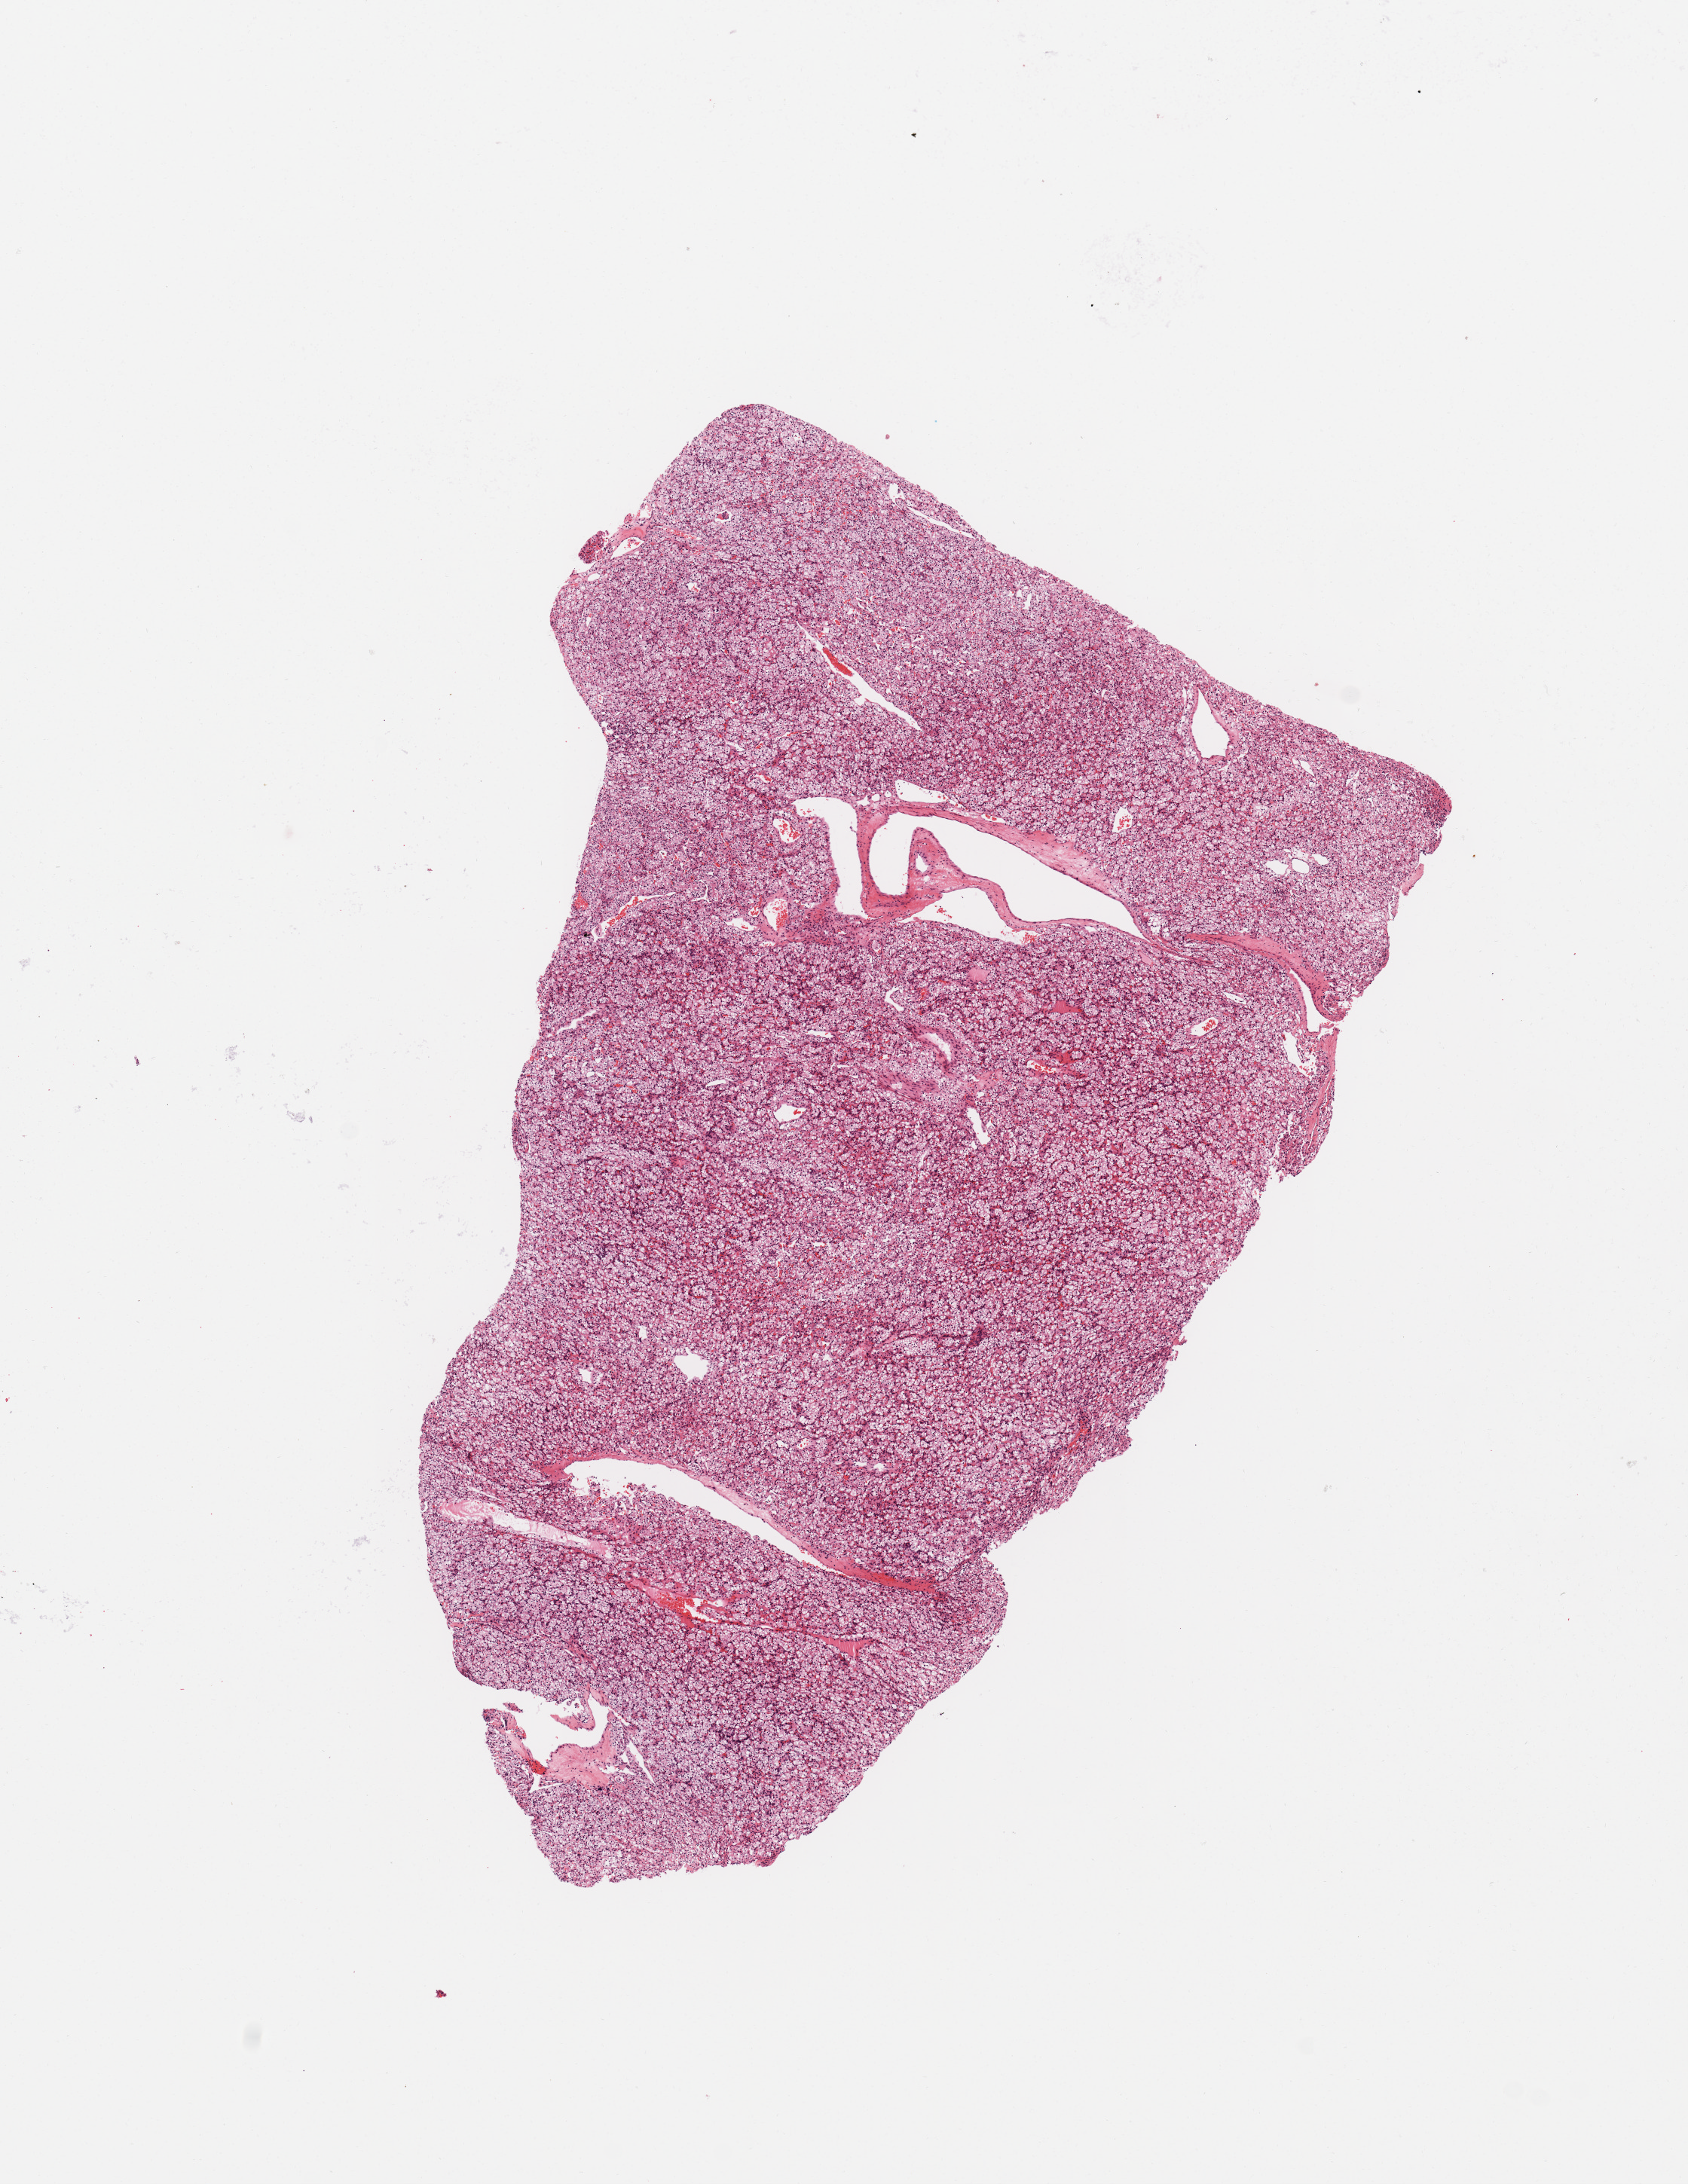
H&E-stained whole-slide image — low-resolution overview of the scanned area, about 8.9 x 11.5 mm, tumour tissue sample, sampled site: kidney. Male, 54 y/o. Histologic grade: G2 (moderately differentiated). Pathologist review of this section (percent, as recorded): tumour nuclei 90%, necrosis 0%.
* AJCC pathologic stage: I
* histologic diagnosis: Renal cell carcinoma, NOS